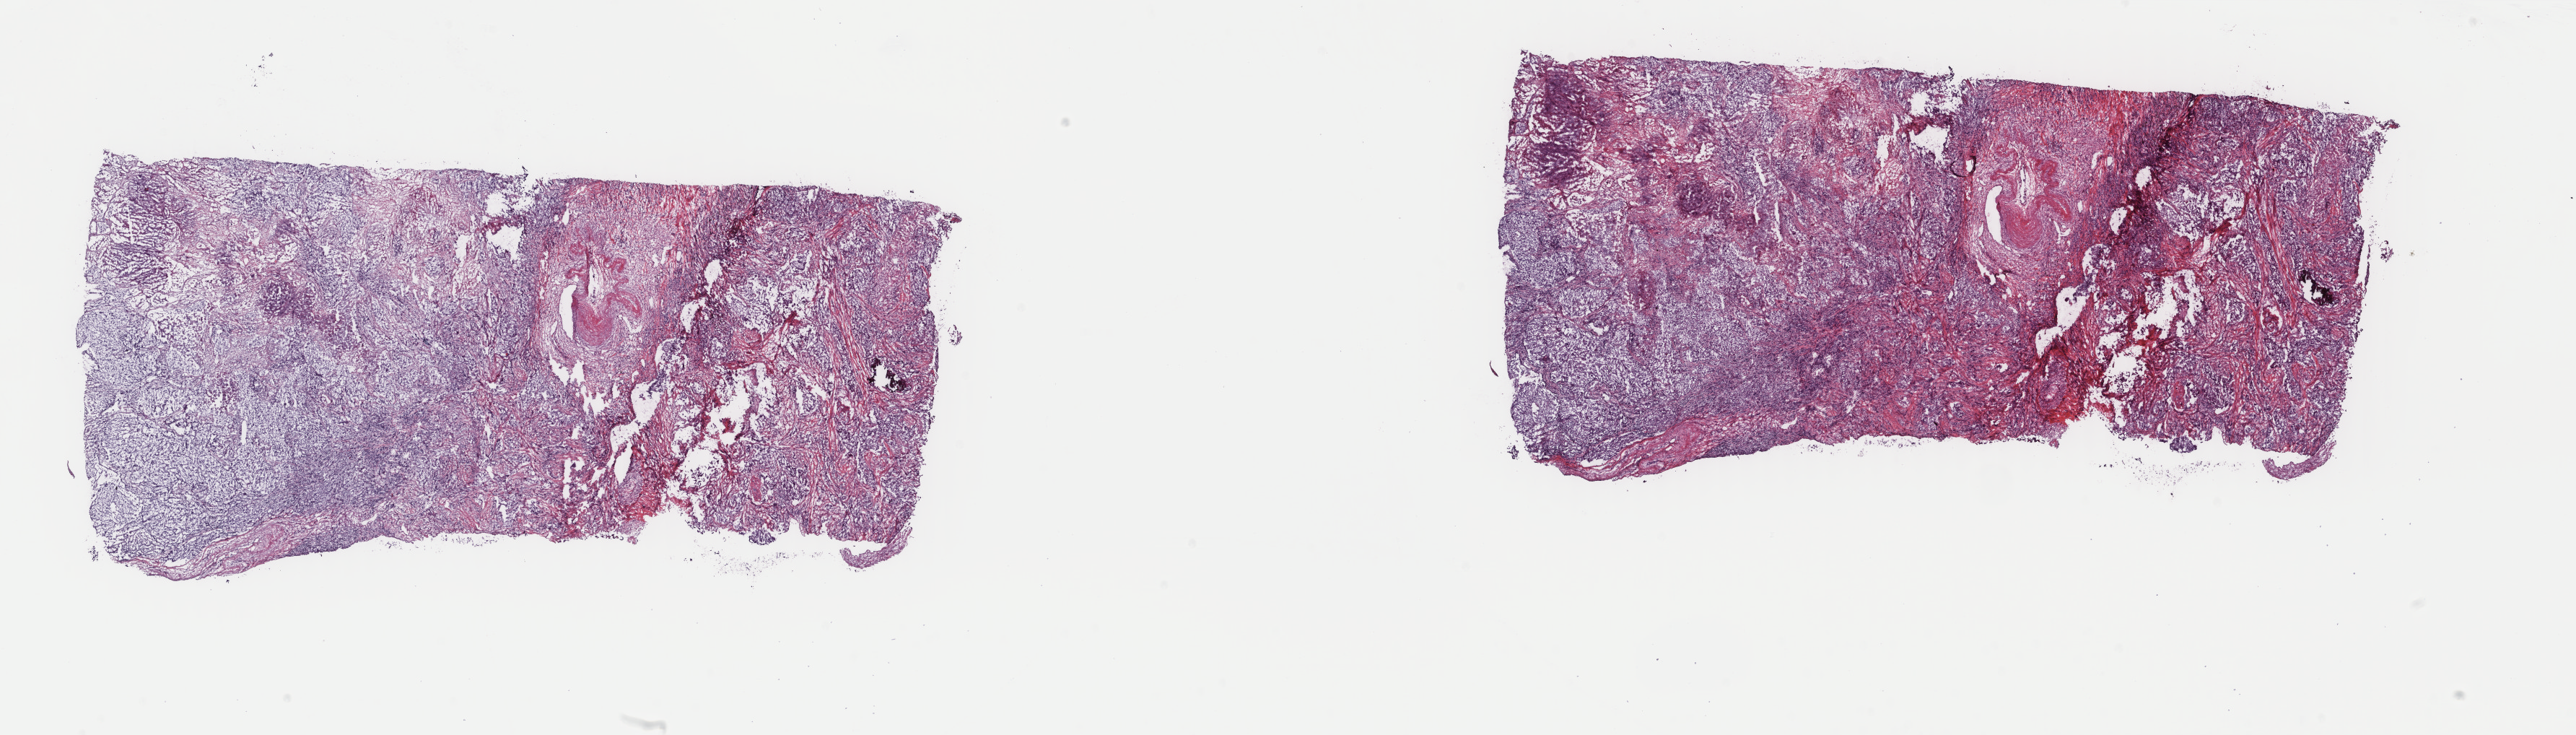
Whole-slide histology image, H&E — low-resolution overview of the scanned area, about 28.3 x 8.1 mm. Frozen section from the top of the tissue portion. Primary tumour sample from the lung. Female, age 68 years at initial diagnosis. Pathologist review of this section (percent, as recorded): tumour cells 85%, tumour nuclei 65%, normal cells 0%, stromal cells 15%, necrosis 0%. Inflammatory infiltration, as recorded: lymphocyte infiltration 0%, monocyte infiltration 0%, neutrophil infiltration 0%.
Histologic diagnosis: Adenocarcinoma, NOS (lower lobe, lung). AJCC pathologic stage: IIB (6th edition). Laterality: right.